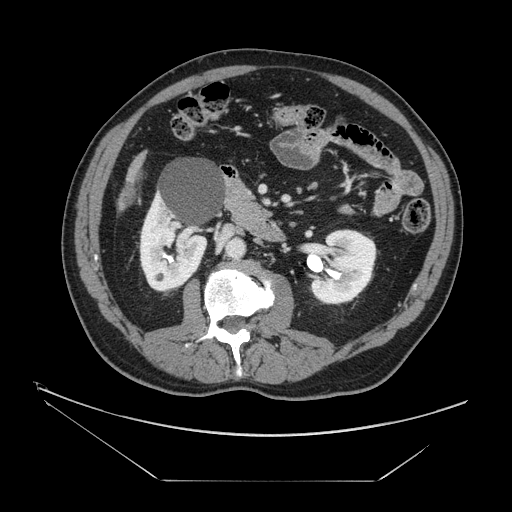
Contrast-enhanced abdominal CT, one axial slice. Slice 48 of 161 in the series (ordered by position). Reconstruction kernel STANDARD. 120 kVp. Soft-tissue window (W 400 / L 40 HU). 2.5 mm slice thickness. 512 × 512 image matrix. Male patient, age 65 years. Case-level facts recorded for this patient, not image findings: diagnosis: colorectal cancer liver metastases, imaged before liver resection; multiple liver metastases: yes; largest metastasis: 4.2 cm.
Structures marked on this image (outlined manually by an expert reader):
- liver: bounding box <134,166,140,174> (left, top, right, bottom; pixels)
- liver metastasis: <123,188,133,204>